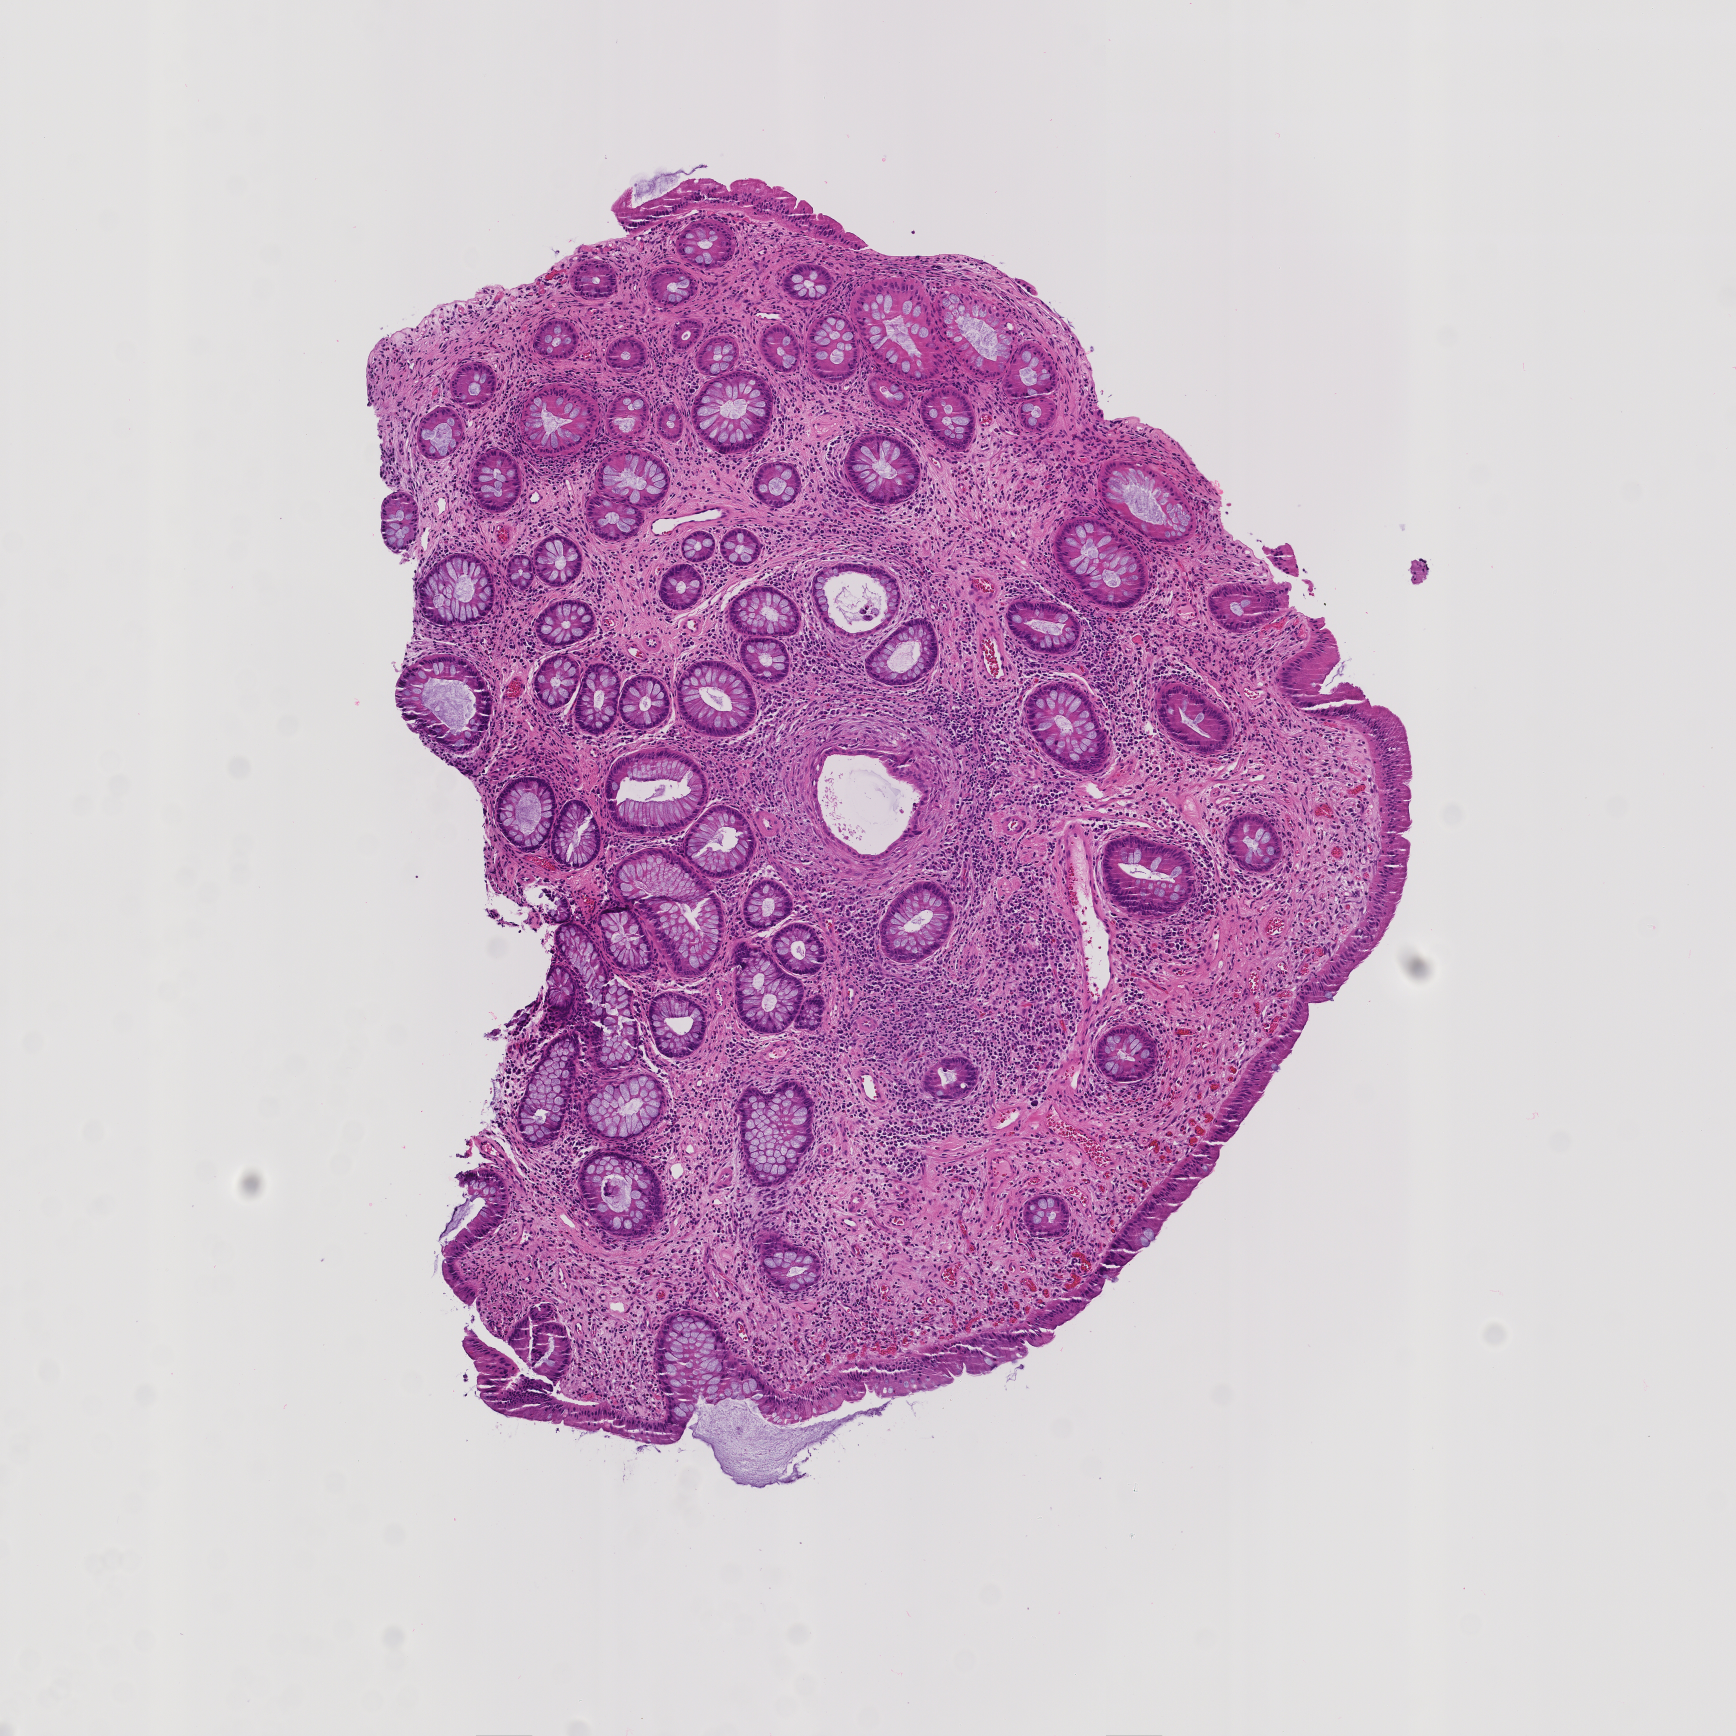
Whole-slide image, H&E stain: colon biopsy — whole scanned area (about 3.5 x 3.5 mm) shown as a low-resolution overview, formalin-fixed, paraffin-embedded (FFPE) tissue, site: sigmoid colon. Patient sex: female.
- lesion category (as recorded): normal (as recorded)